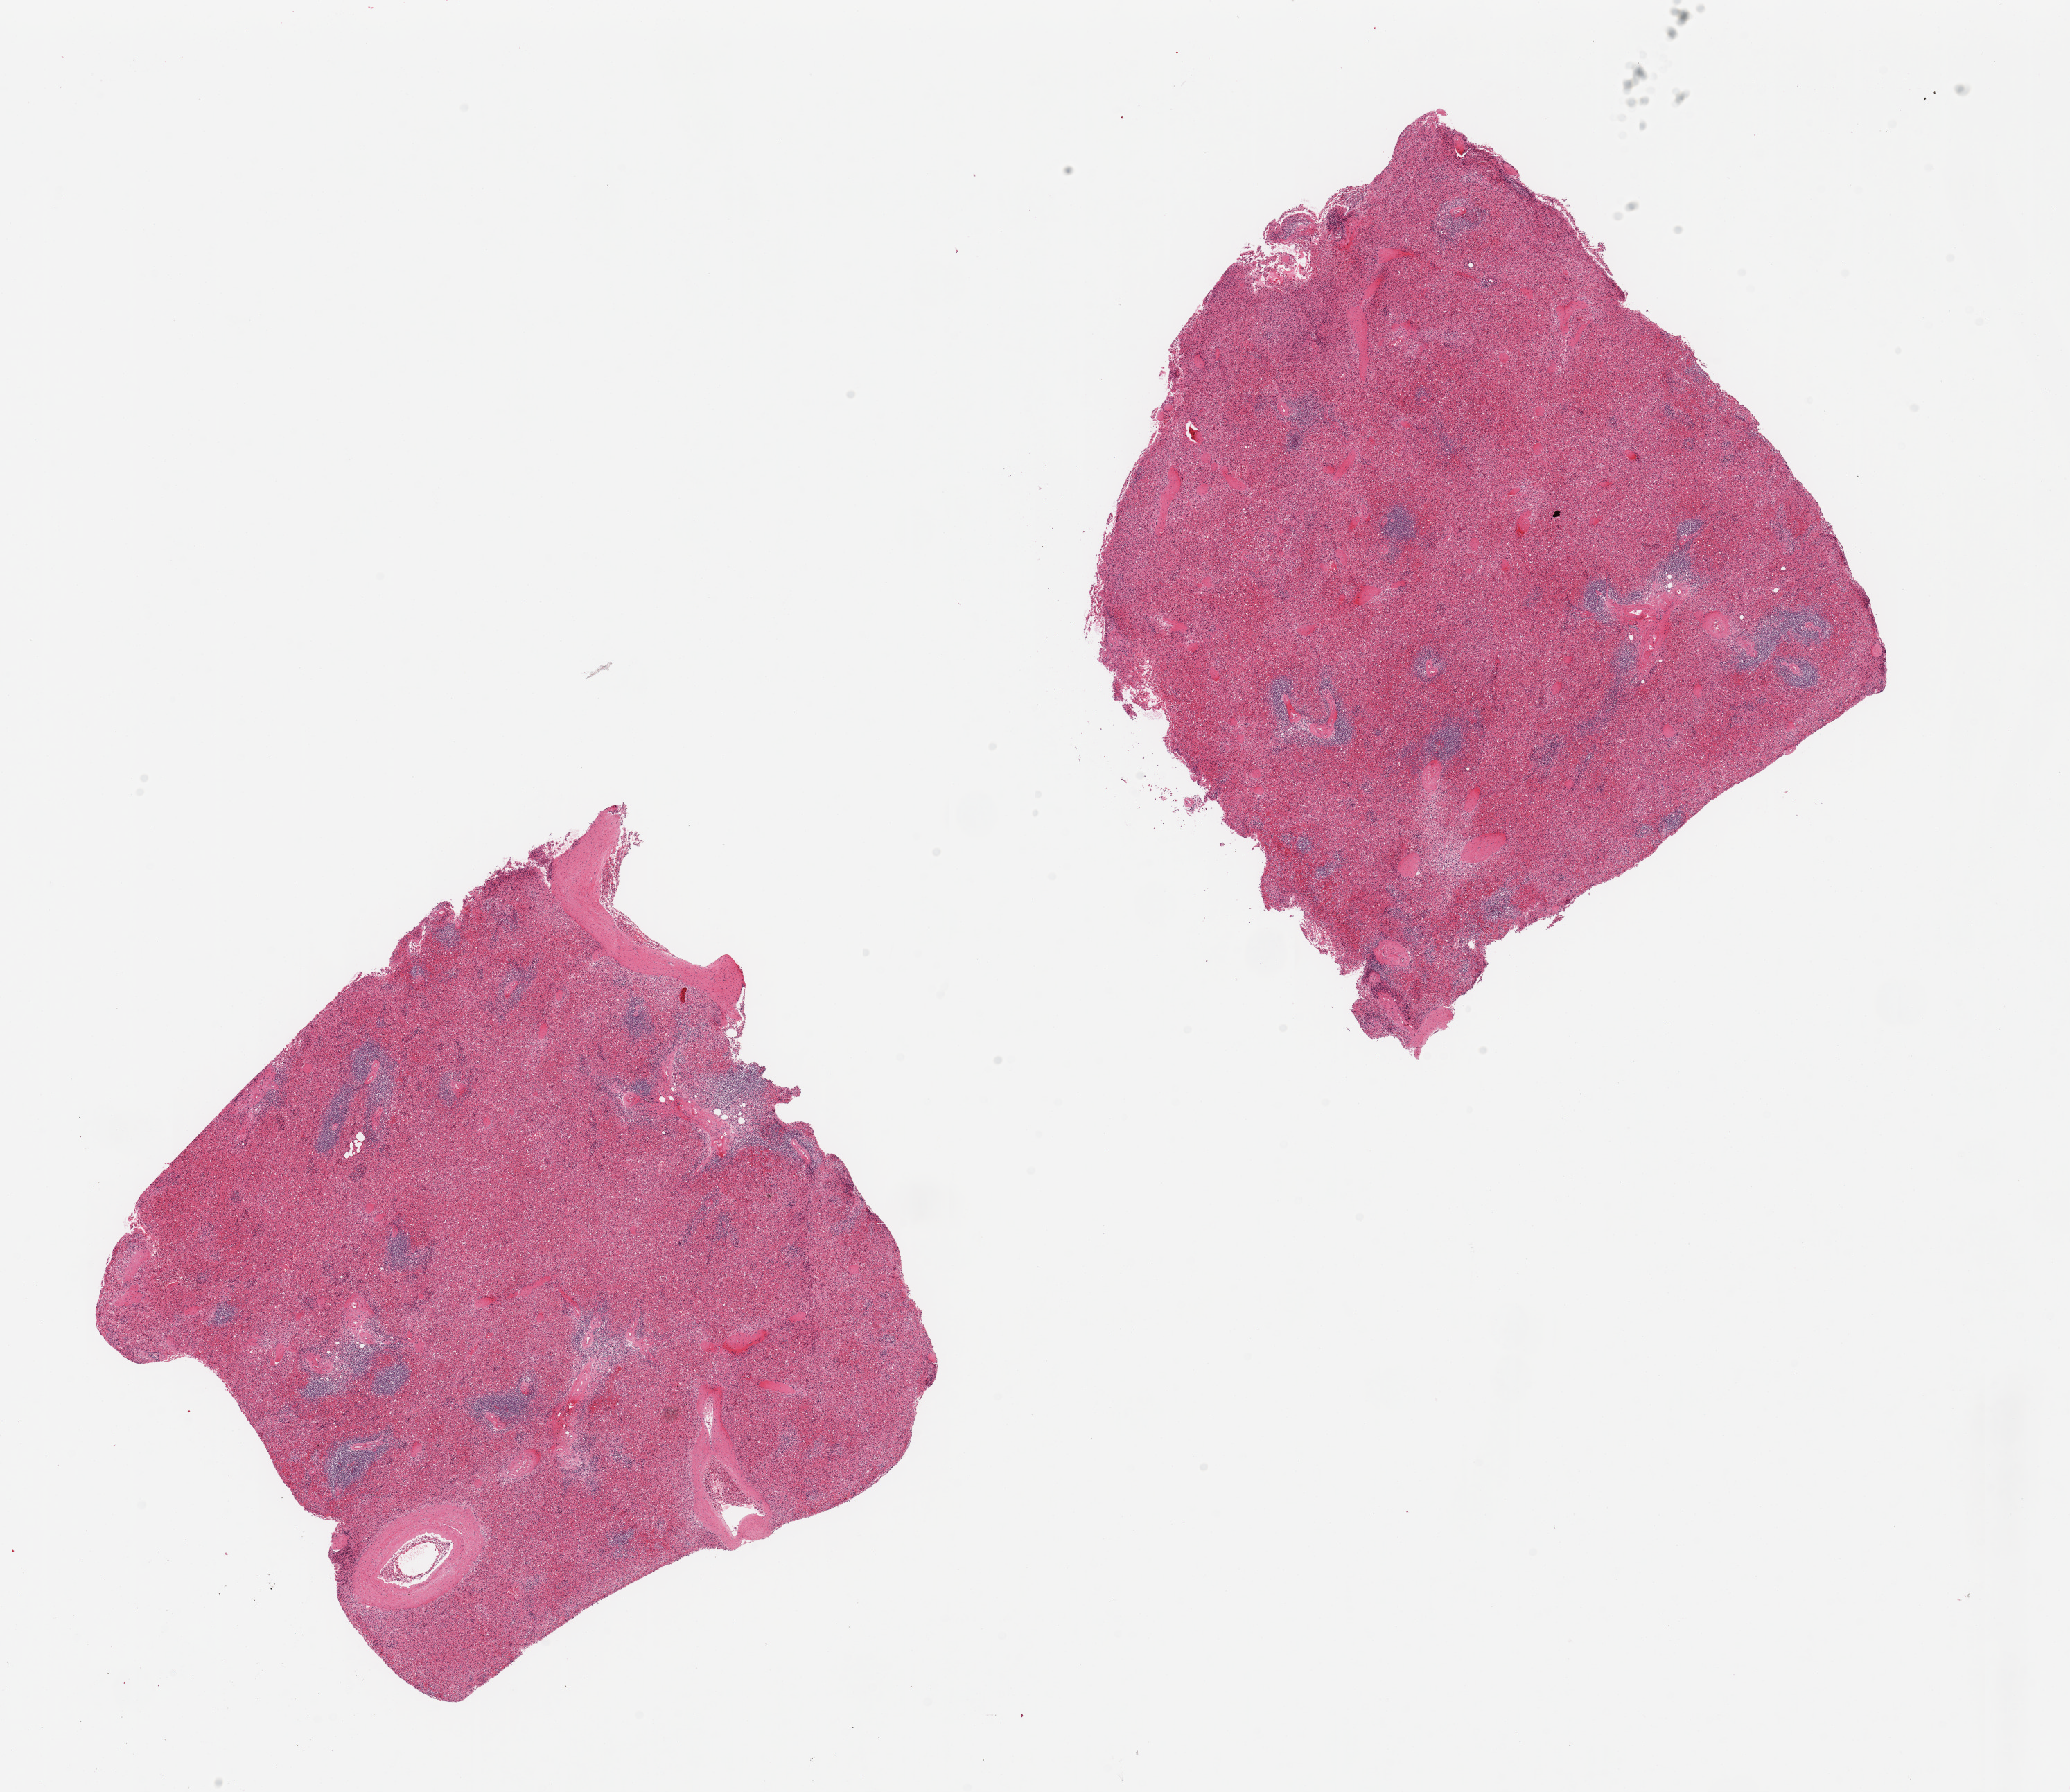
Whole-slide image, H&E stain — shown as a low-resolution overview of the whole scanned area (about 23.6 x 20.5 mm, from a 20x scan), PAXgene-fixed paraffin-embedded (PFPE) section, section of spleen (target tissue), donor tissue sample. Donor: male.
Pathologist's review note for this sample: 2 pieces; focal congestion.